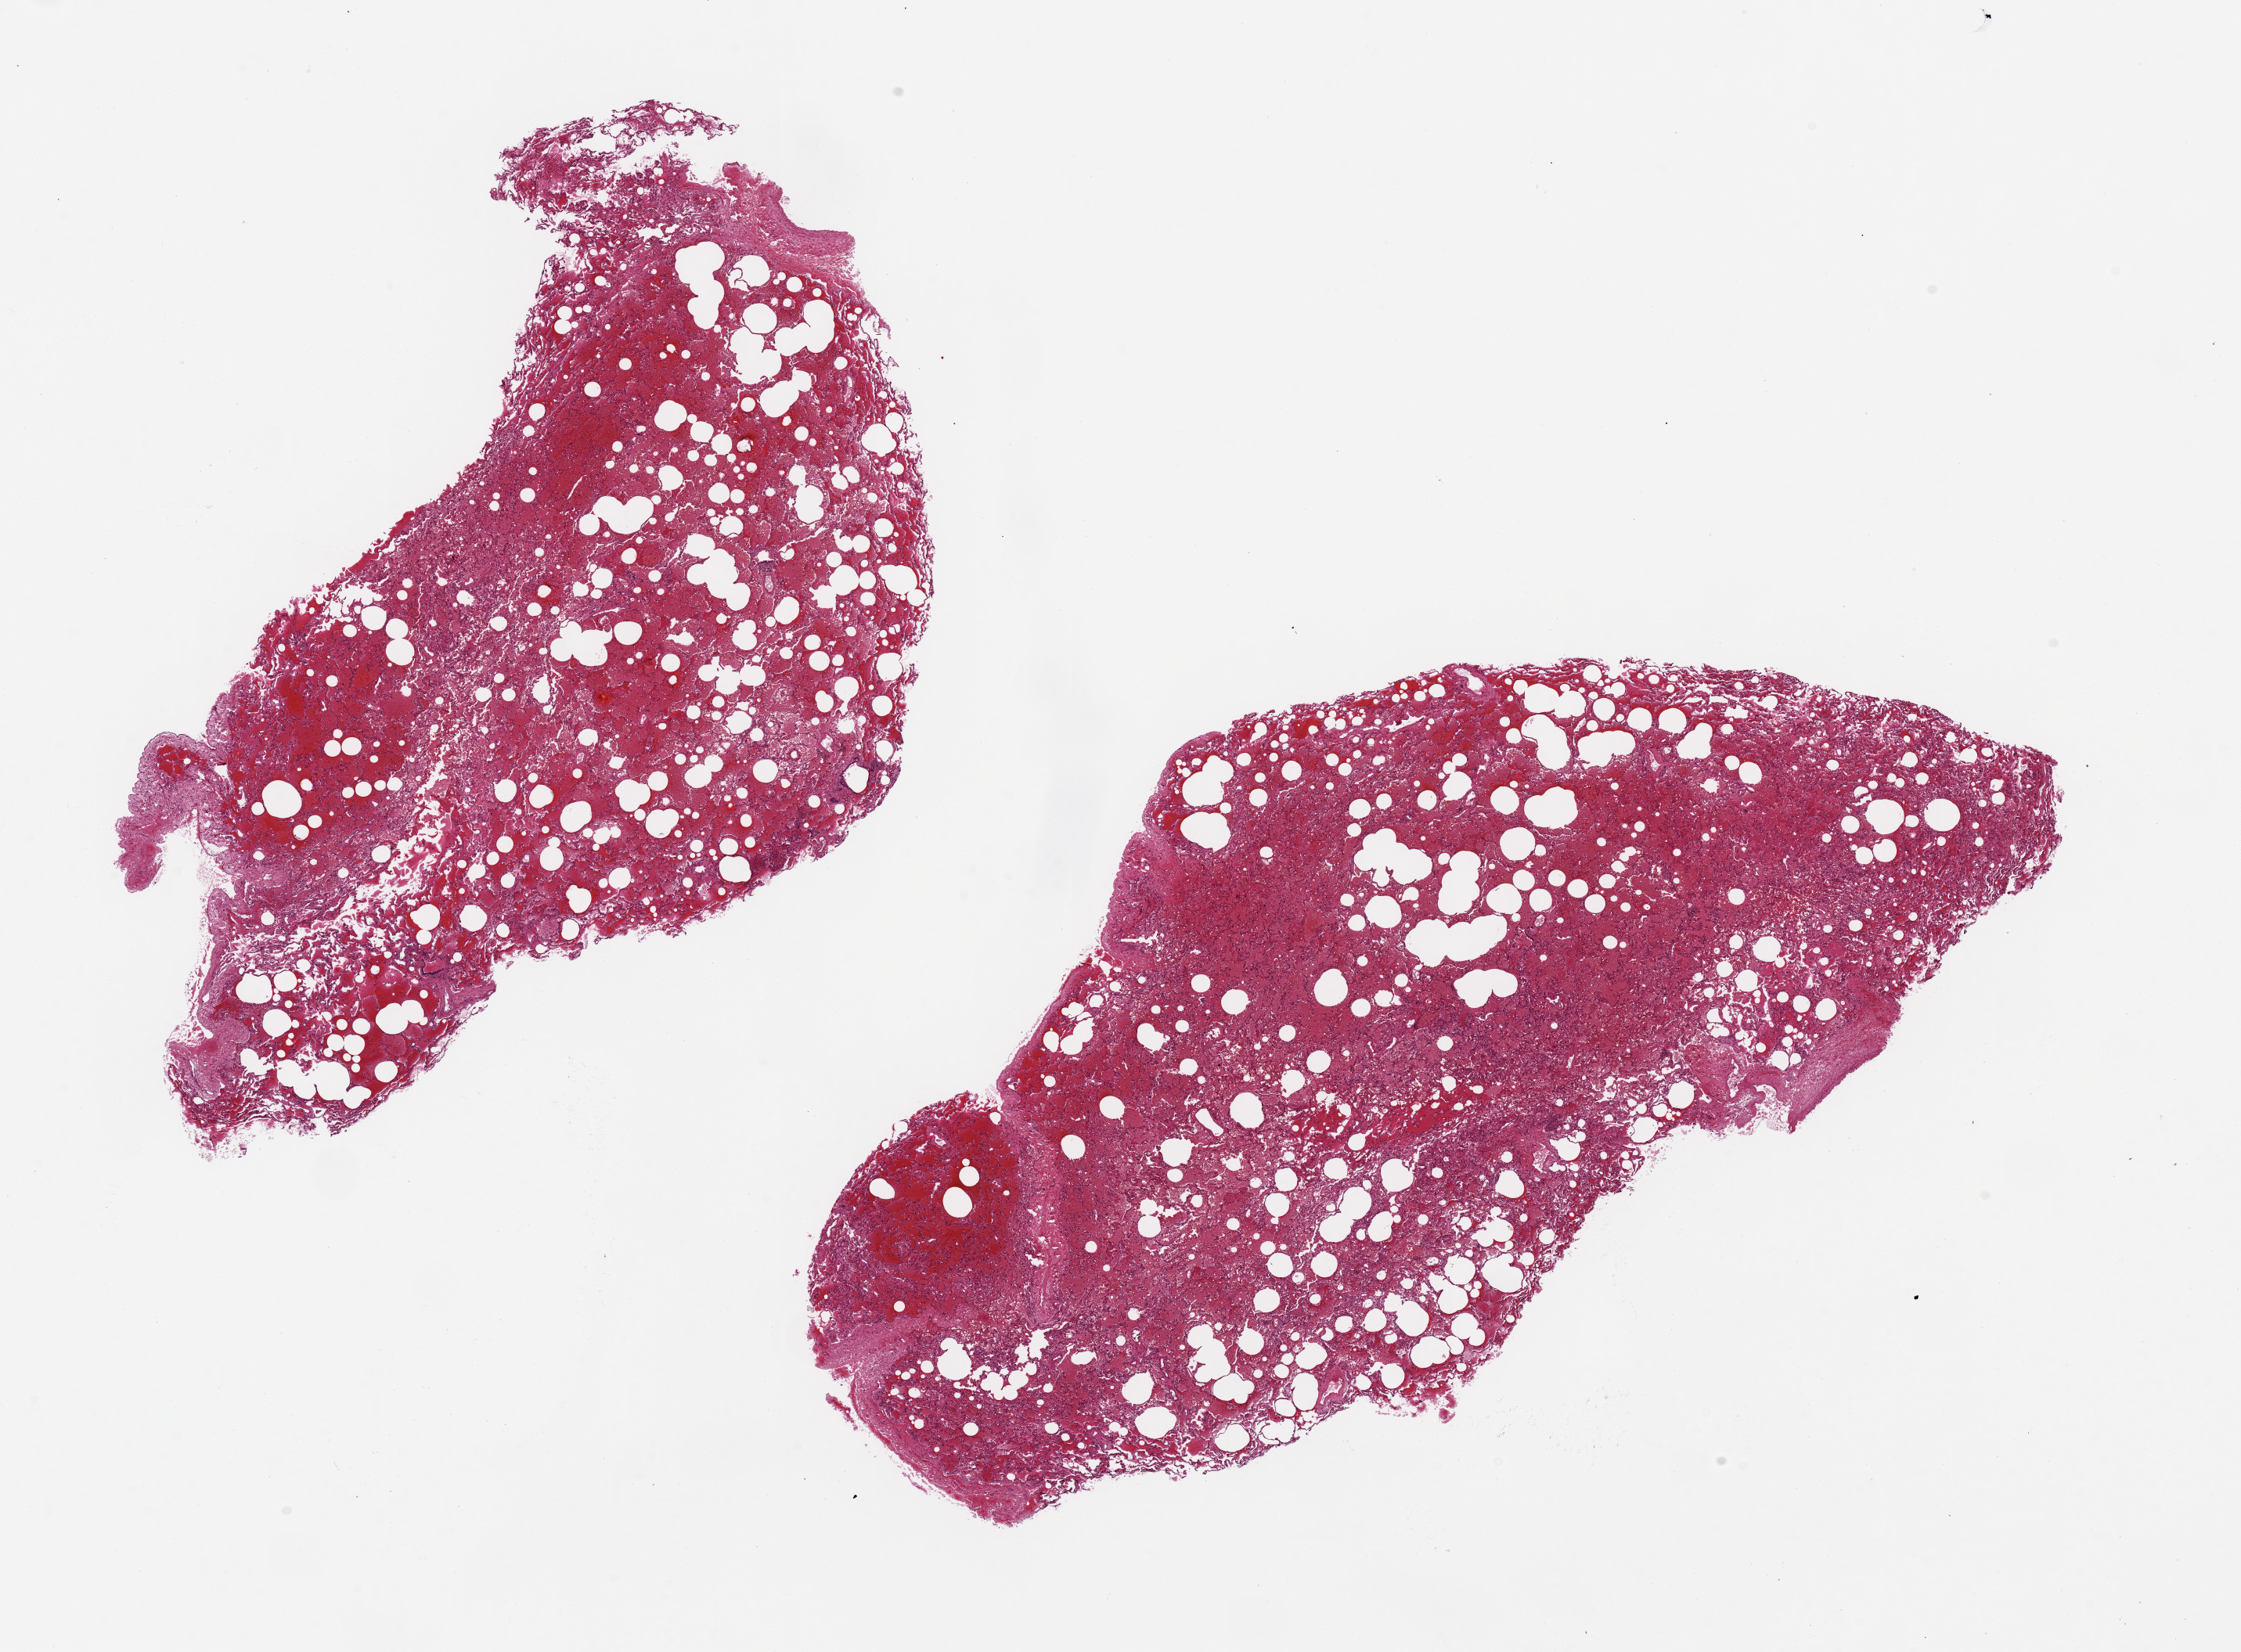
Digitized hematoxylin and eosin (H&E)-stained section, brightfield — shown as a low-resolution overview of the whole scanned area (about 22.6 x 16.7 mm), PAXgene-fixed, paraffin-embedded tissue, sampled site (target tissue): lung, tissue donor sample. Donor: female.
Pathologist's review note for this sample: 2 pieces, ~8x8mm. Diffuse intra-alveolar hemorrhage but minimal inflammation.